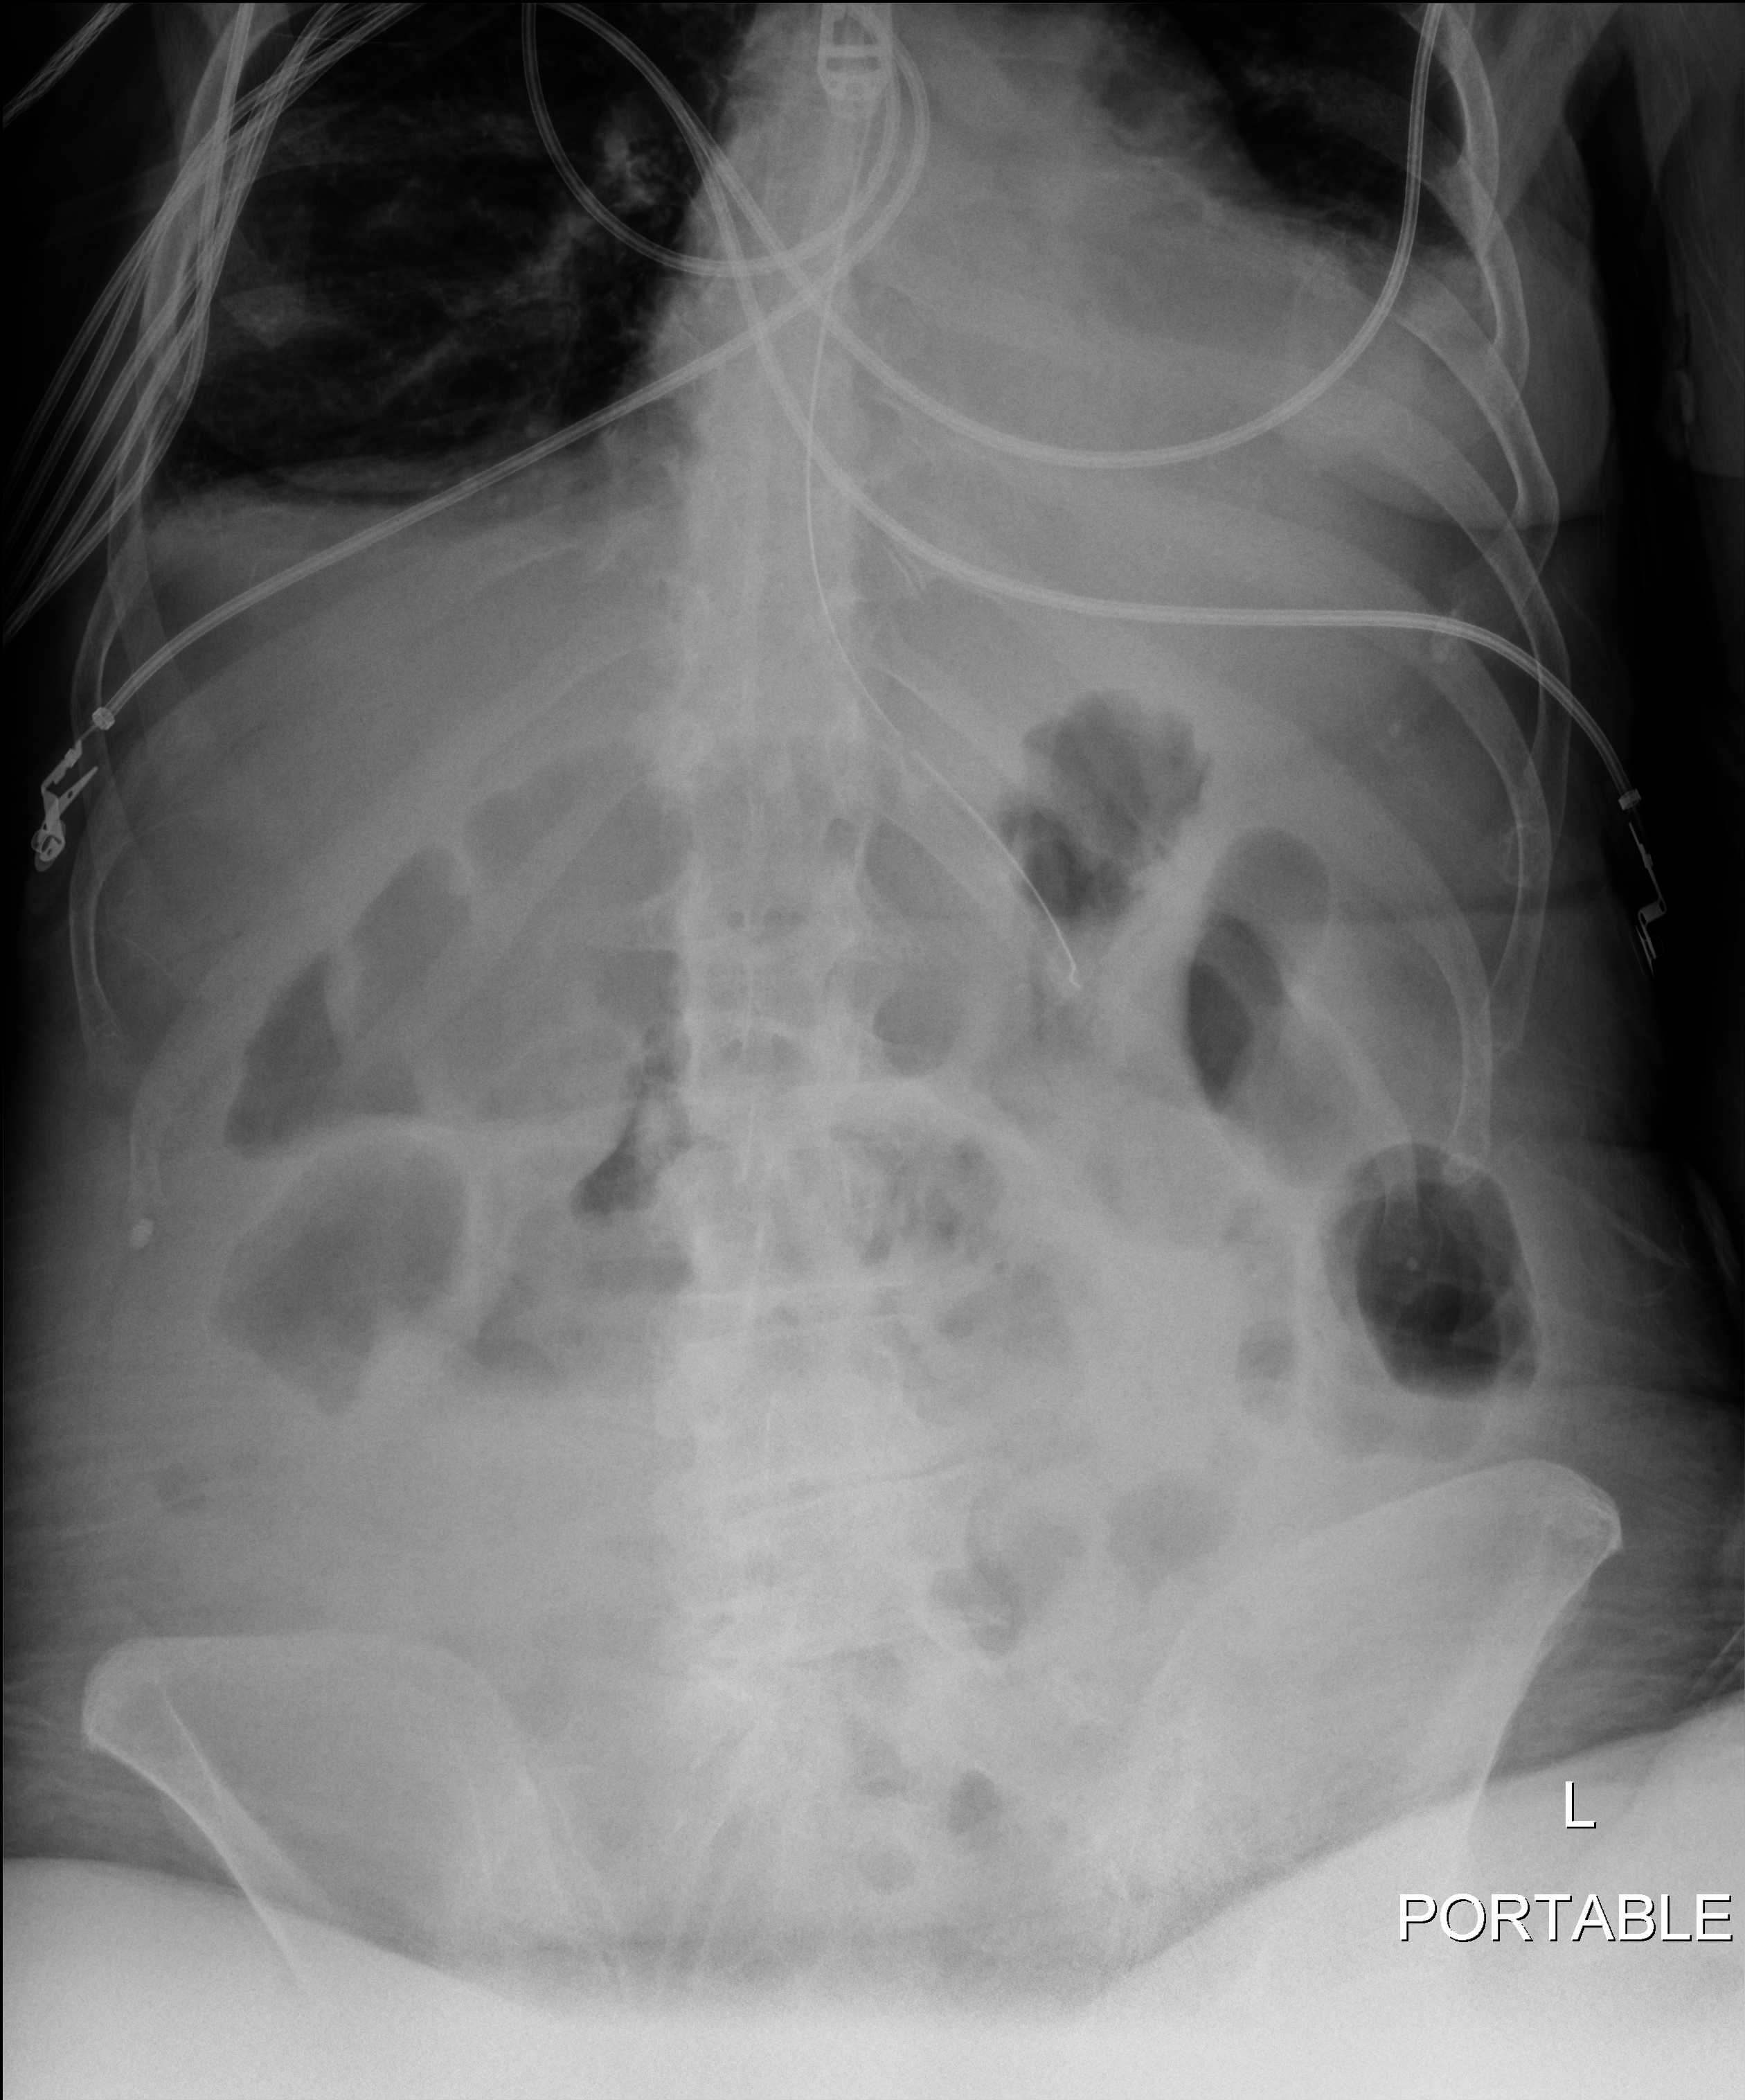
Portable abdomen radiograph; anteroposterior (AP) projection. Patient hospitalised with COVID-19; female, aged 60–74 years.
Admission-level facts for this patient (not findings on this image; timing relative to this image not recorded):
- mechanically ventilated during this hospital stay: yes
- admitted to intensive care during this hospital stay: yes